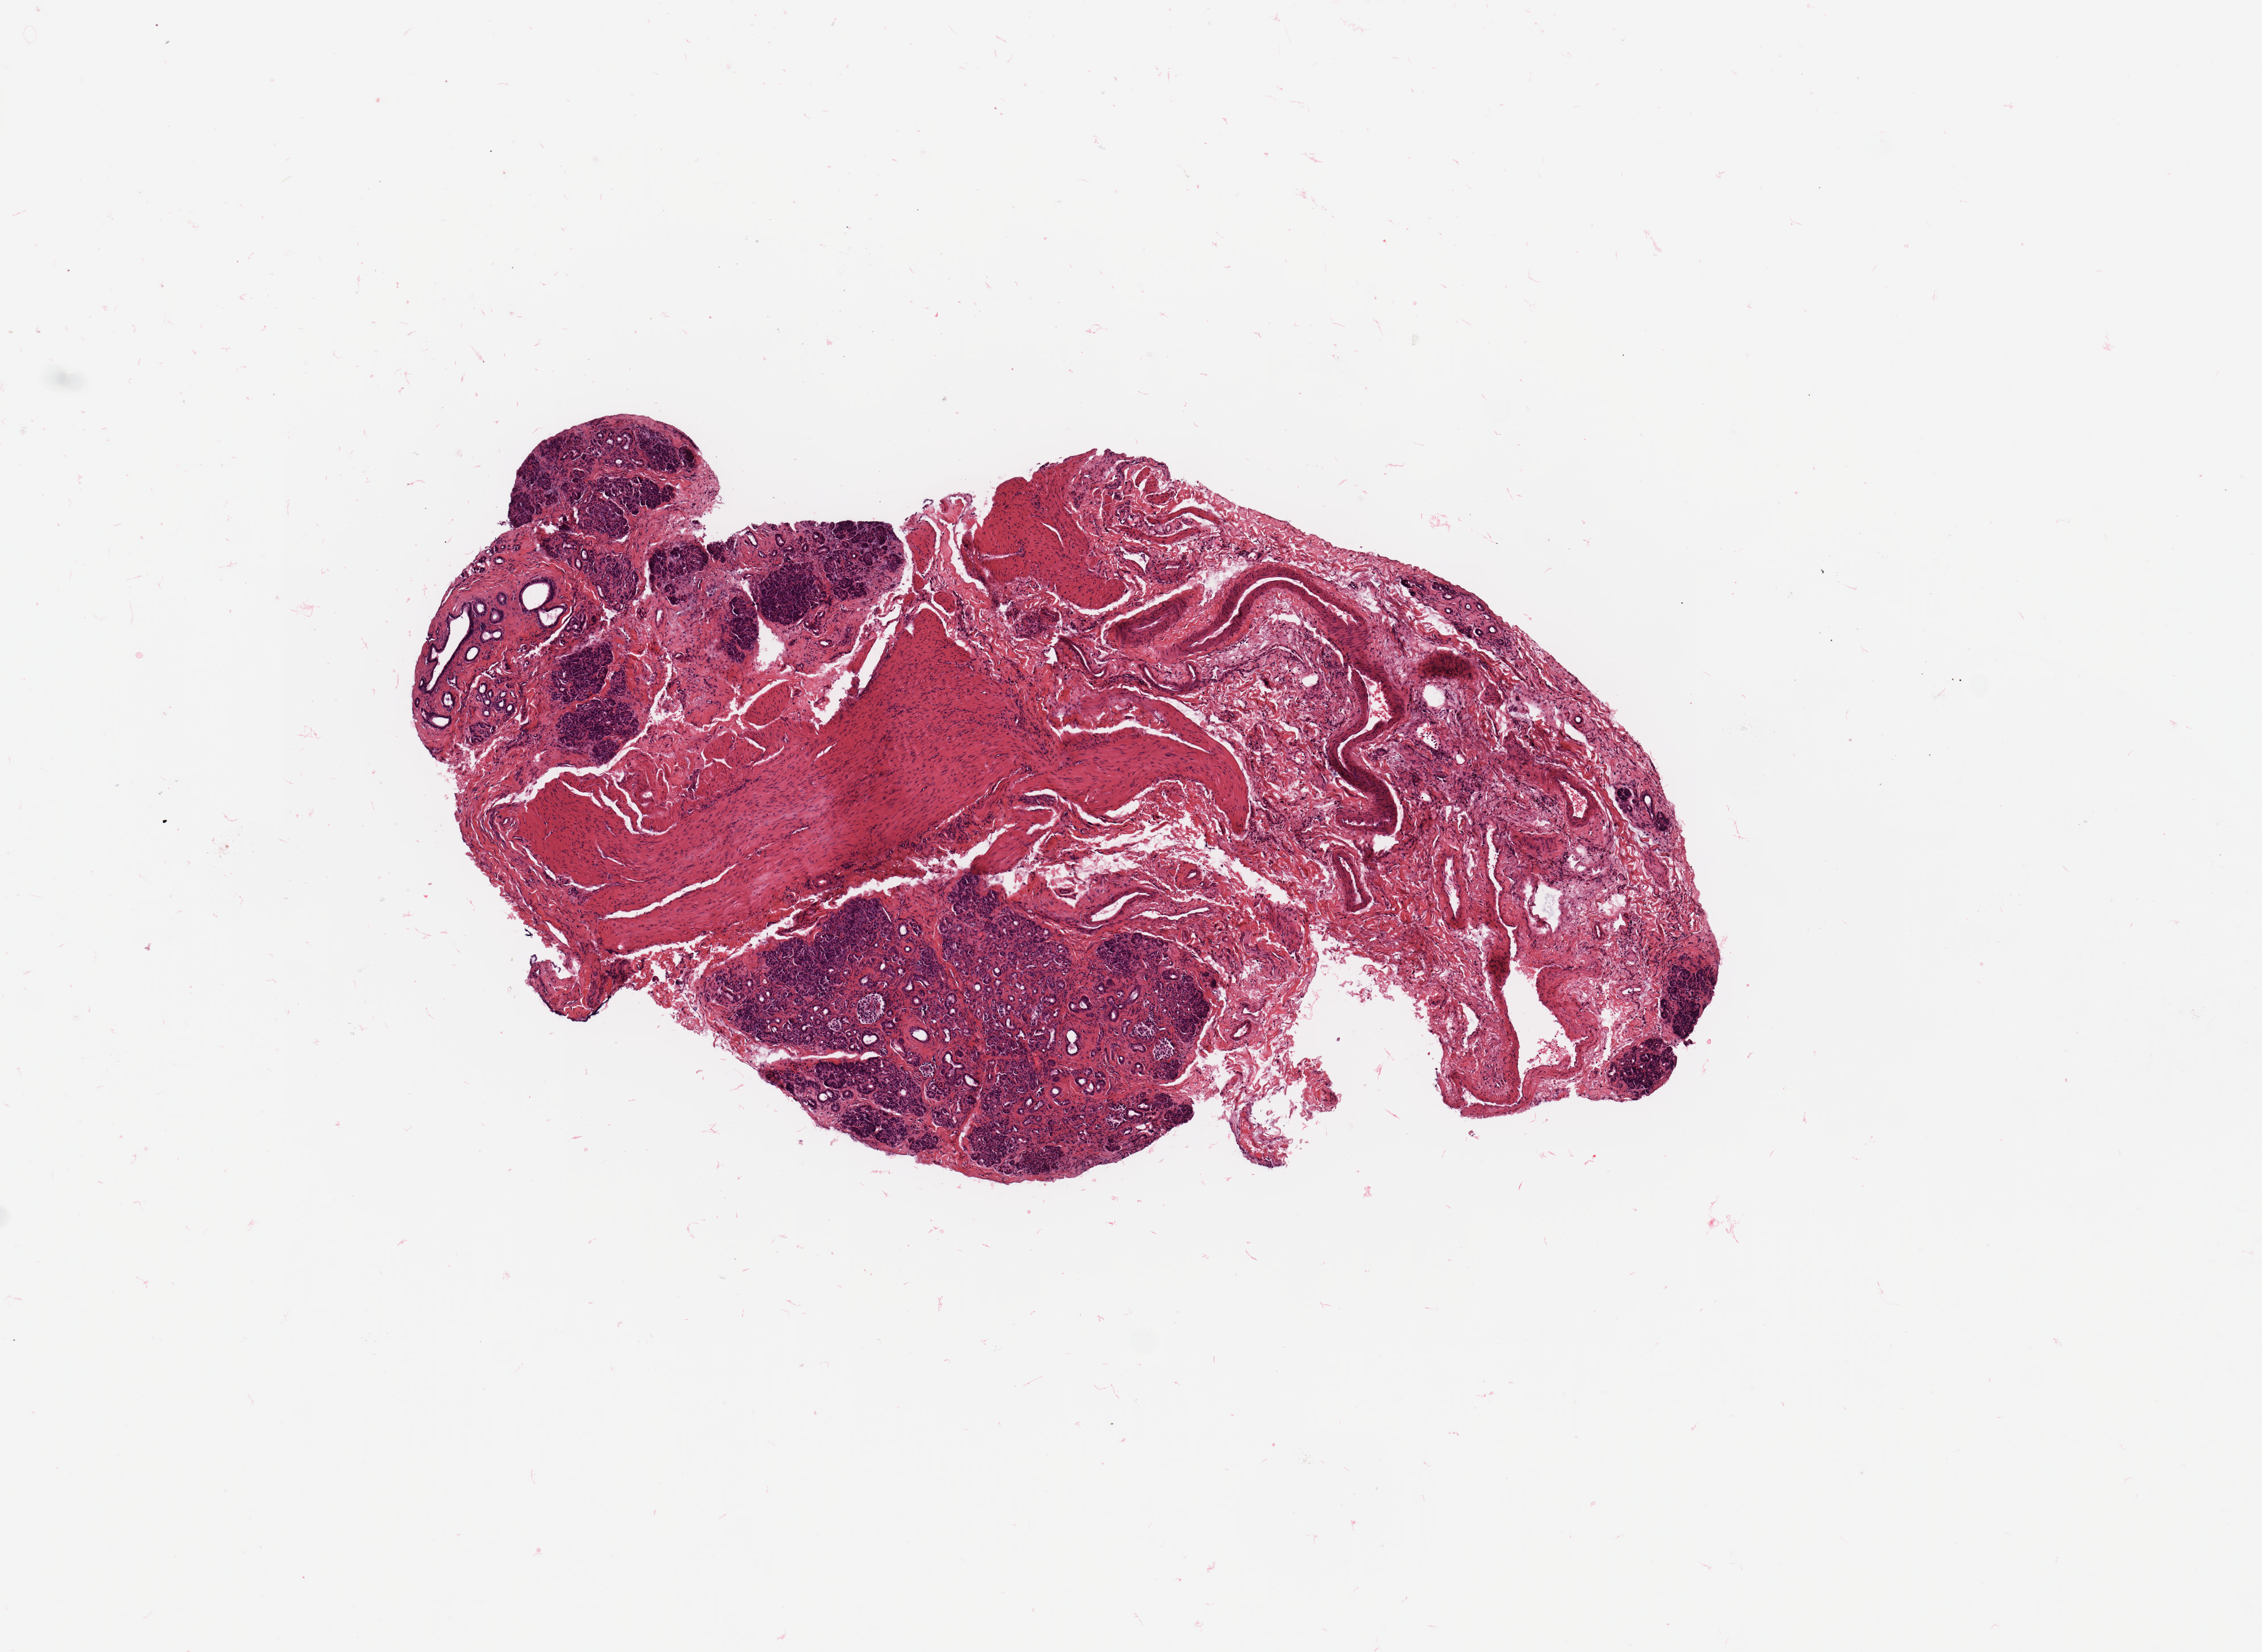
Digitized H&E tissue section (whole slide), whole scanned area (about 7.9 x 5.8 mm, slide scanned at 20x) shown as a low-resolution overview; pancreas, normal (non-tumour) tissue. 66-year-old male patient.
- this section: normal (non-tumour) tissue from the same patient
- patient diagnosis: Infiltrating duct carcinoma, NOS